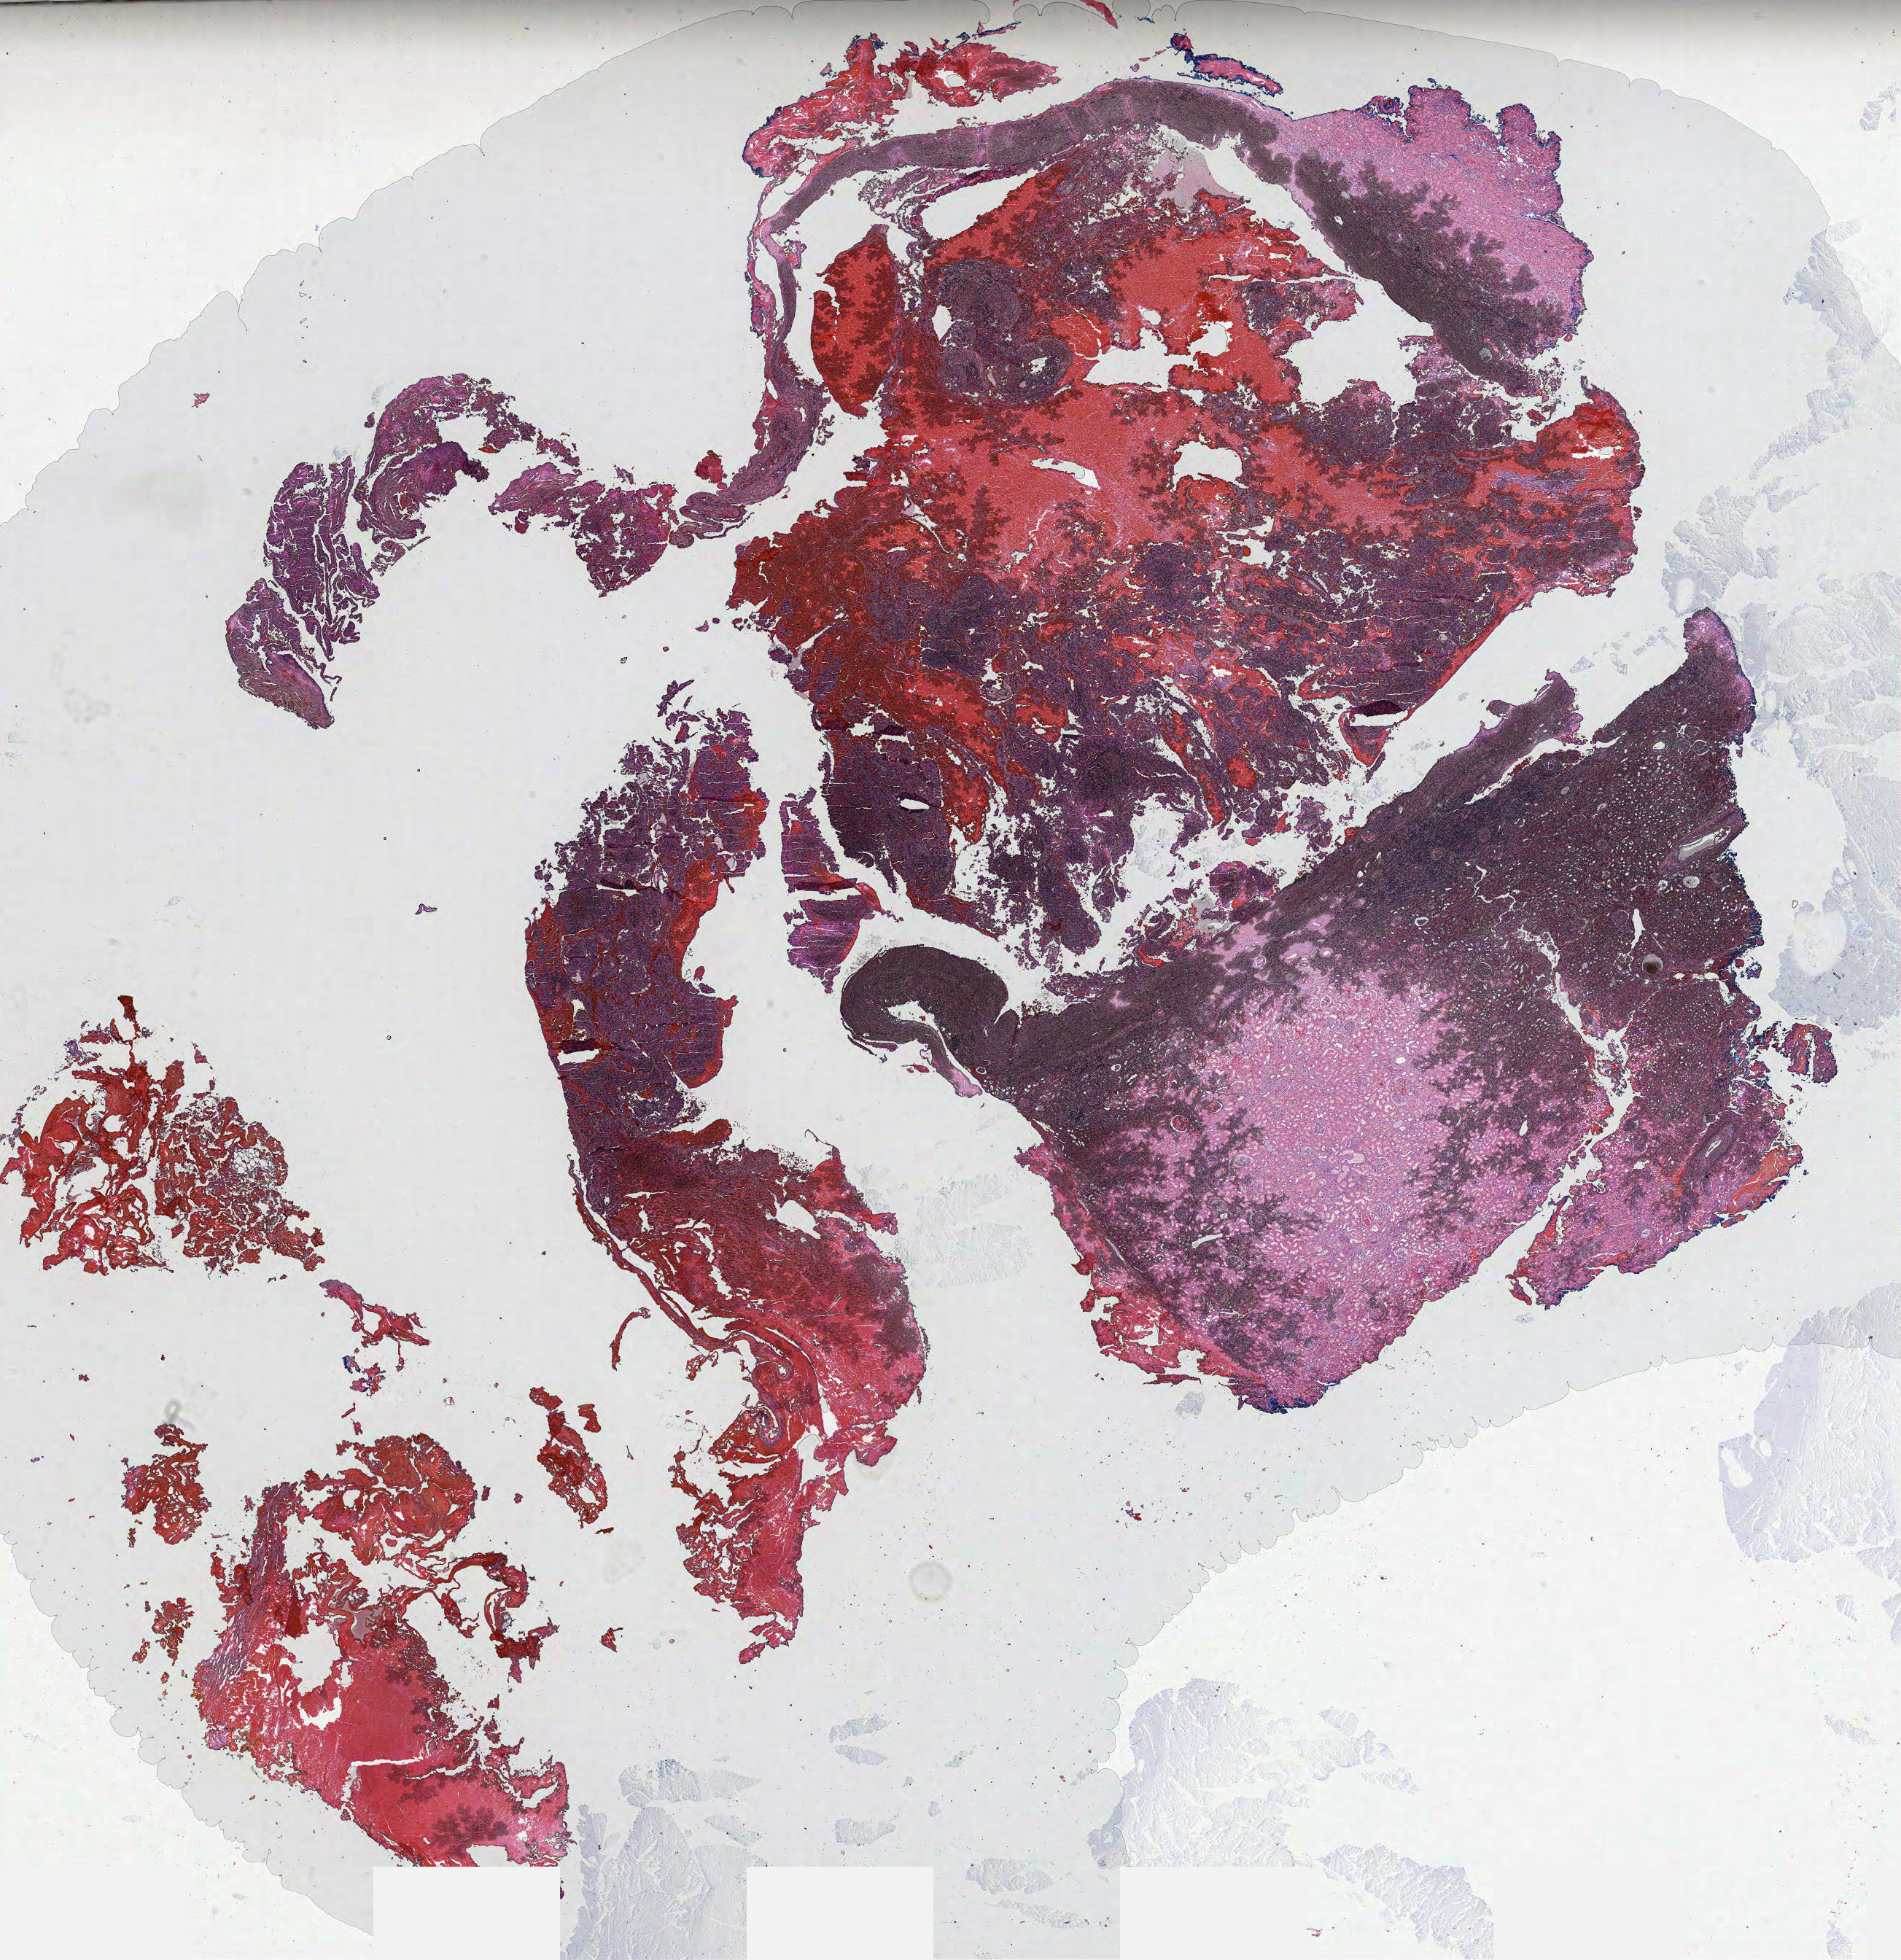
Digitized Hematoxylin and eosin (H&E) stained tissue section (whole slide), shown as a low-resolution overview of the whole scanned area (about 21.0 x 21.7 mm, slide scanned at 40x). Formalin-fixed paraffin-embedded (FFPE) diagnostic section. Sample: primary tumour, kidney. Patient: male, age at initial diagnosis 71 years.
Laterality: right. AJCC pathologic stage: I. Diagnosis: Papillary adenocarcinoma, NOS.